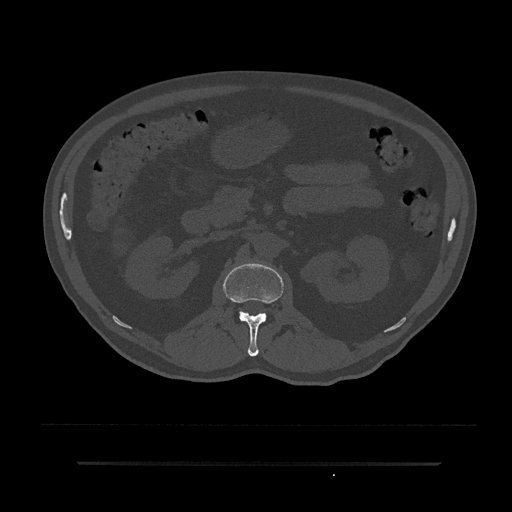
CT including the spine, one axial slice. Position 127 of 797 along the scan axis. Reconstruction kernel Br40s/3. 120 kVp. Bone window (W 1800 / L 400 HU). 0.5 mm slice thickness. 512 × 512 image matrix, field of view 464 × 464 mm. Patient: male, 59 years. Case-level facts recorded for this patient, not image findings: primary cancer: bile ducts; vertebrae with lytic lesions (as recorded): T10.
Annotated regions visible in this slice (semi-automatically segmented with operator editing):
- L1 vertebra: bounding box <223,263,283,357> (left, top, right, bottom; pixels)